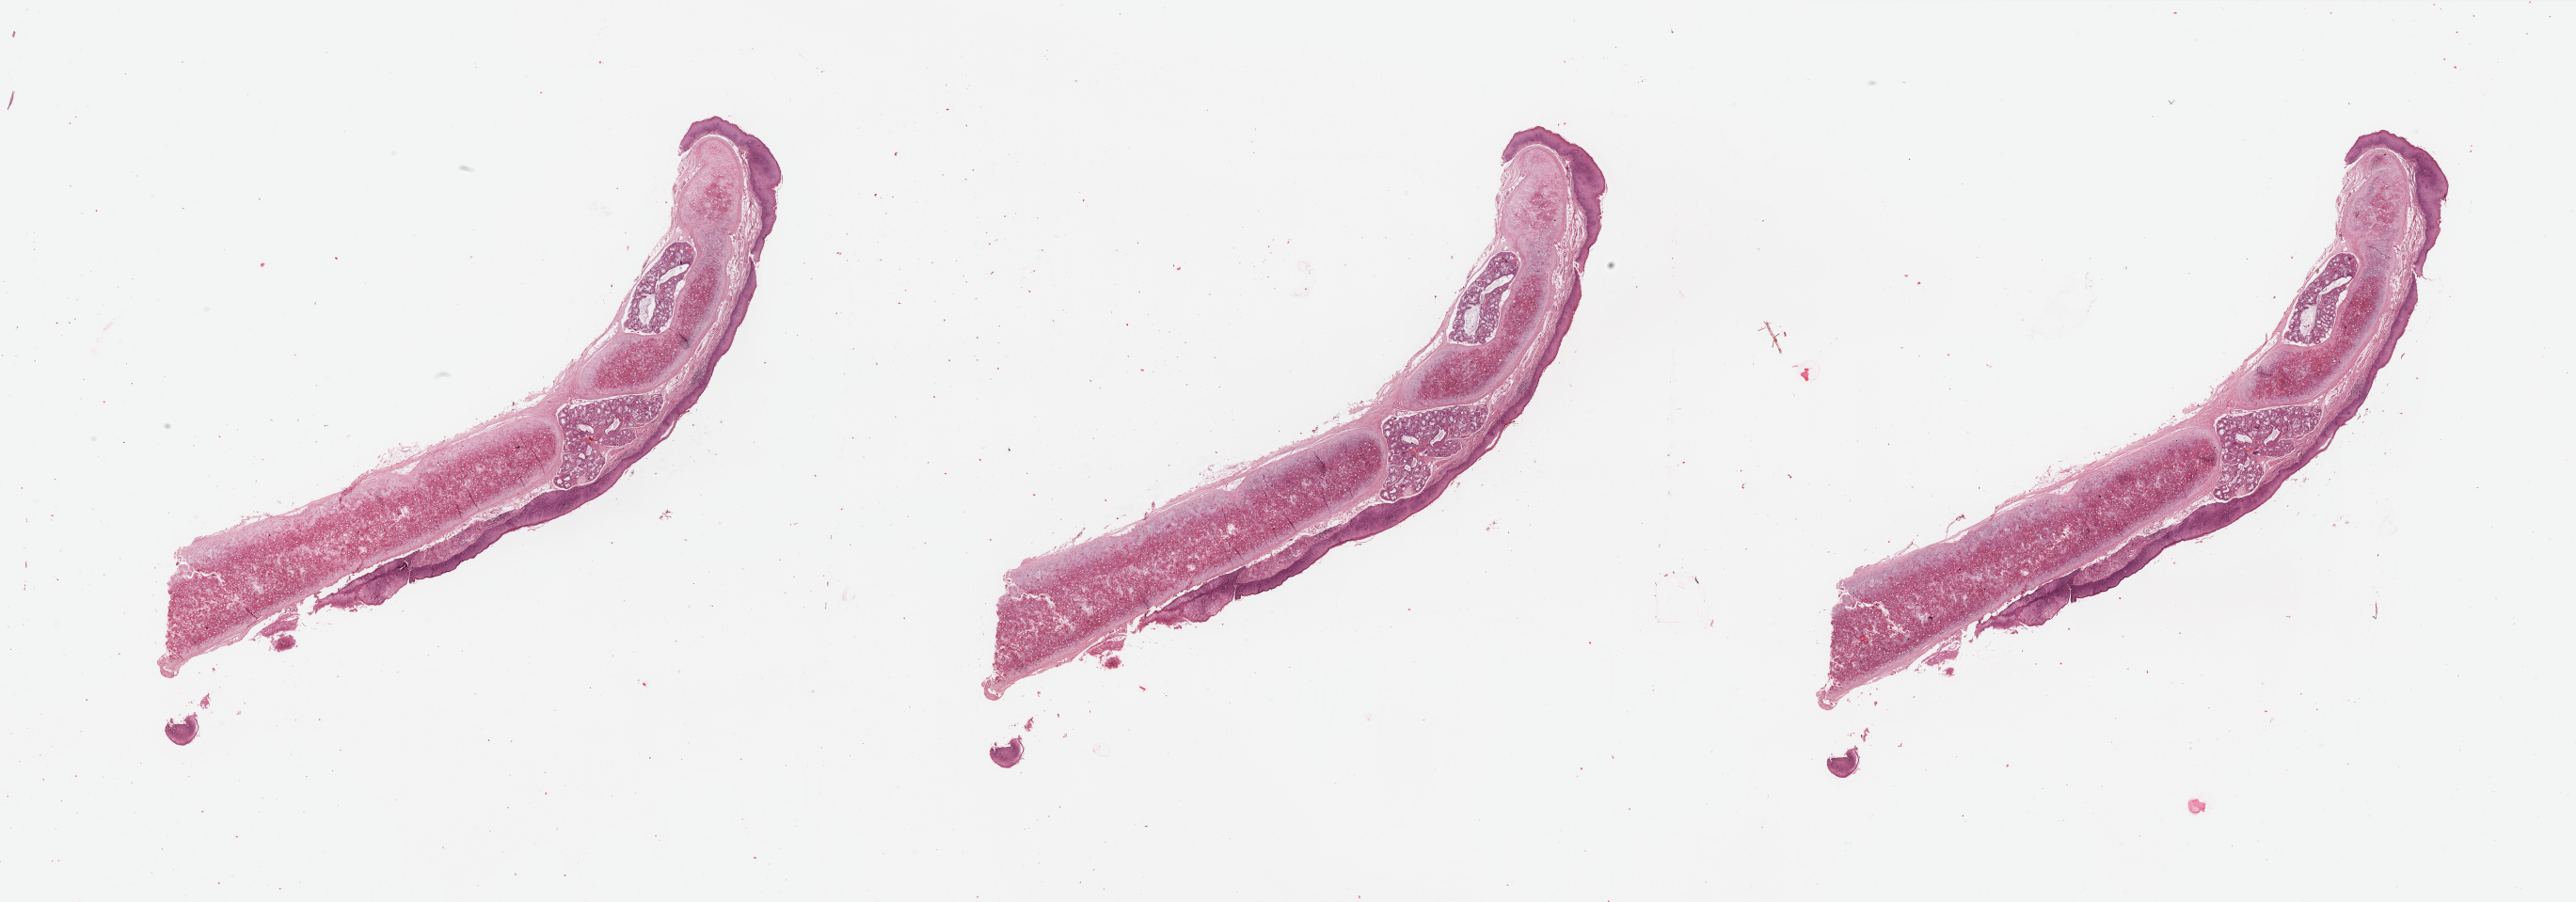
H&E whole-slide image — low-resolution overview of the scanned area, about 43.3 x 15.2 mm (acquisition: 20x scan); head and neck, tissue type not recorded. Patient: male, age 64 years.
* patient diagnosis: Squamous cell carcinoma, NOS (larynx, NOS)